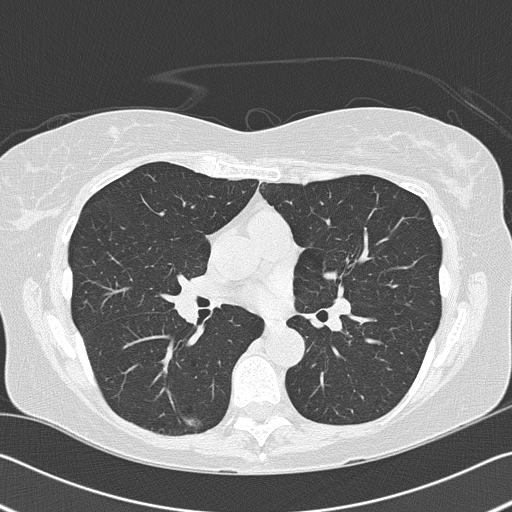
Low-dose screening chest CT, axial slice. First (baseline) screen. Lung window (W 1500 / L -600 HU). 2 mm slice thickness. 512 × 512 image matrix. Female, age 60 years at enrolment. Former smoker at enrolment.
Lesion marked by an expert reader, bounding box <171,408,217,445> (left, top, right, bottom; pixels). The screening reader recorded 2 non-calcified nodules or masses ≥4 mm on this exam; which of them this box marks is not recorded. Later outcome: lung cancer diagnosed 799 days after this screen (after the third annual screen) — acinar cell carcinoma, right lower lobe, moderately differentiated (G2), stage IA (AJCC 6th edition), 10 mm at pathology.